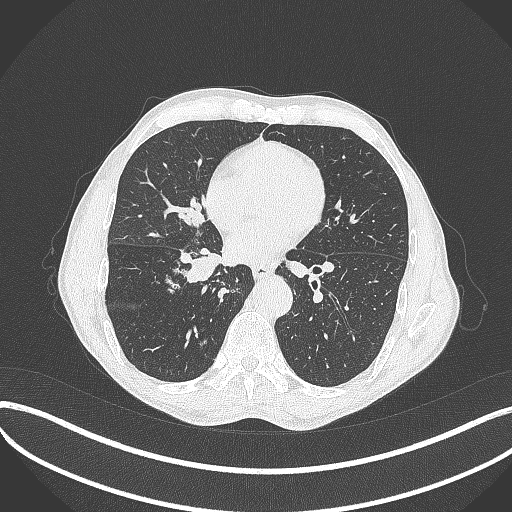
Chest CT, one axial slice. Position 191 of 481 along the scan axis. Reconstruction kernel B70f. Lung window (W 1500 / L -600 HU). 1 mm slice thickness. 512 × 512 image matrix. Patient: male, 65 years. Case-level facts recorded for this patient, not image findings: clinical TNM (as recorded): T2a N0 M0; histopathological grade: G2.
Structures marked on this image (rectangle marked by the reading radiologist):
- lung tumour (recorded histology: squamous cell carcinoma): bounding box (x1, y1, x2, y2) in pixels: (173, 243, 226, 288)